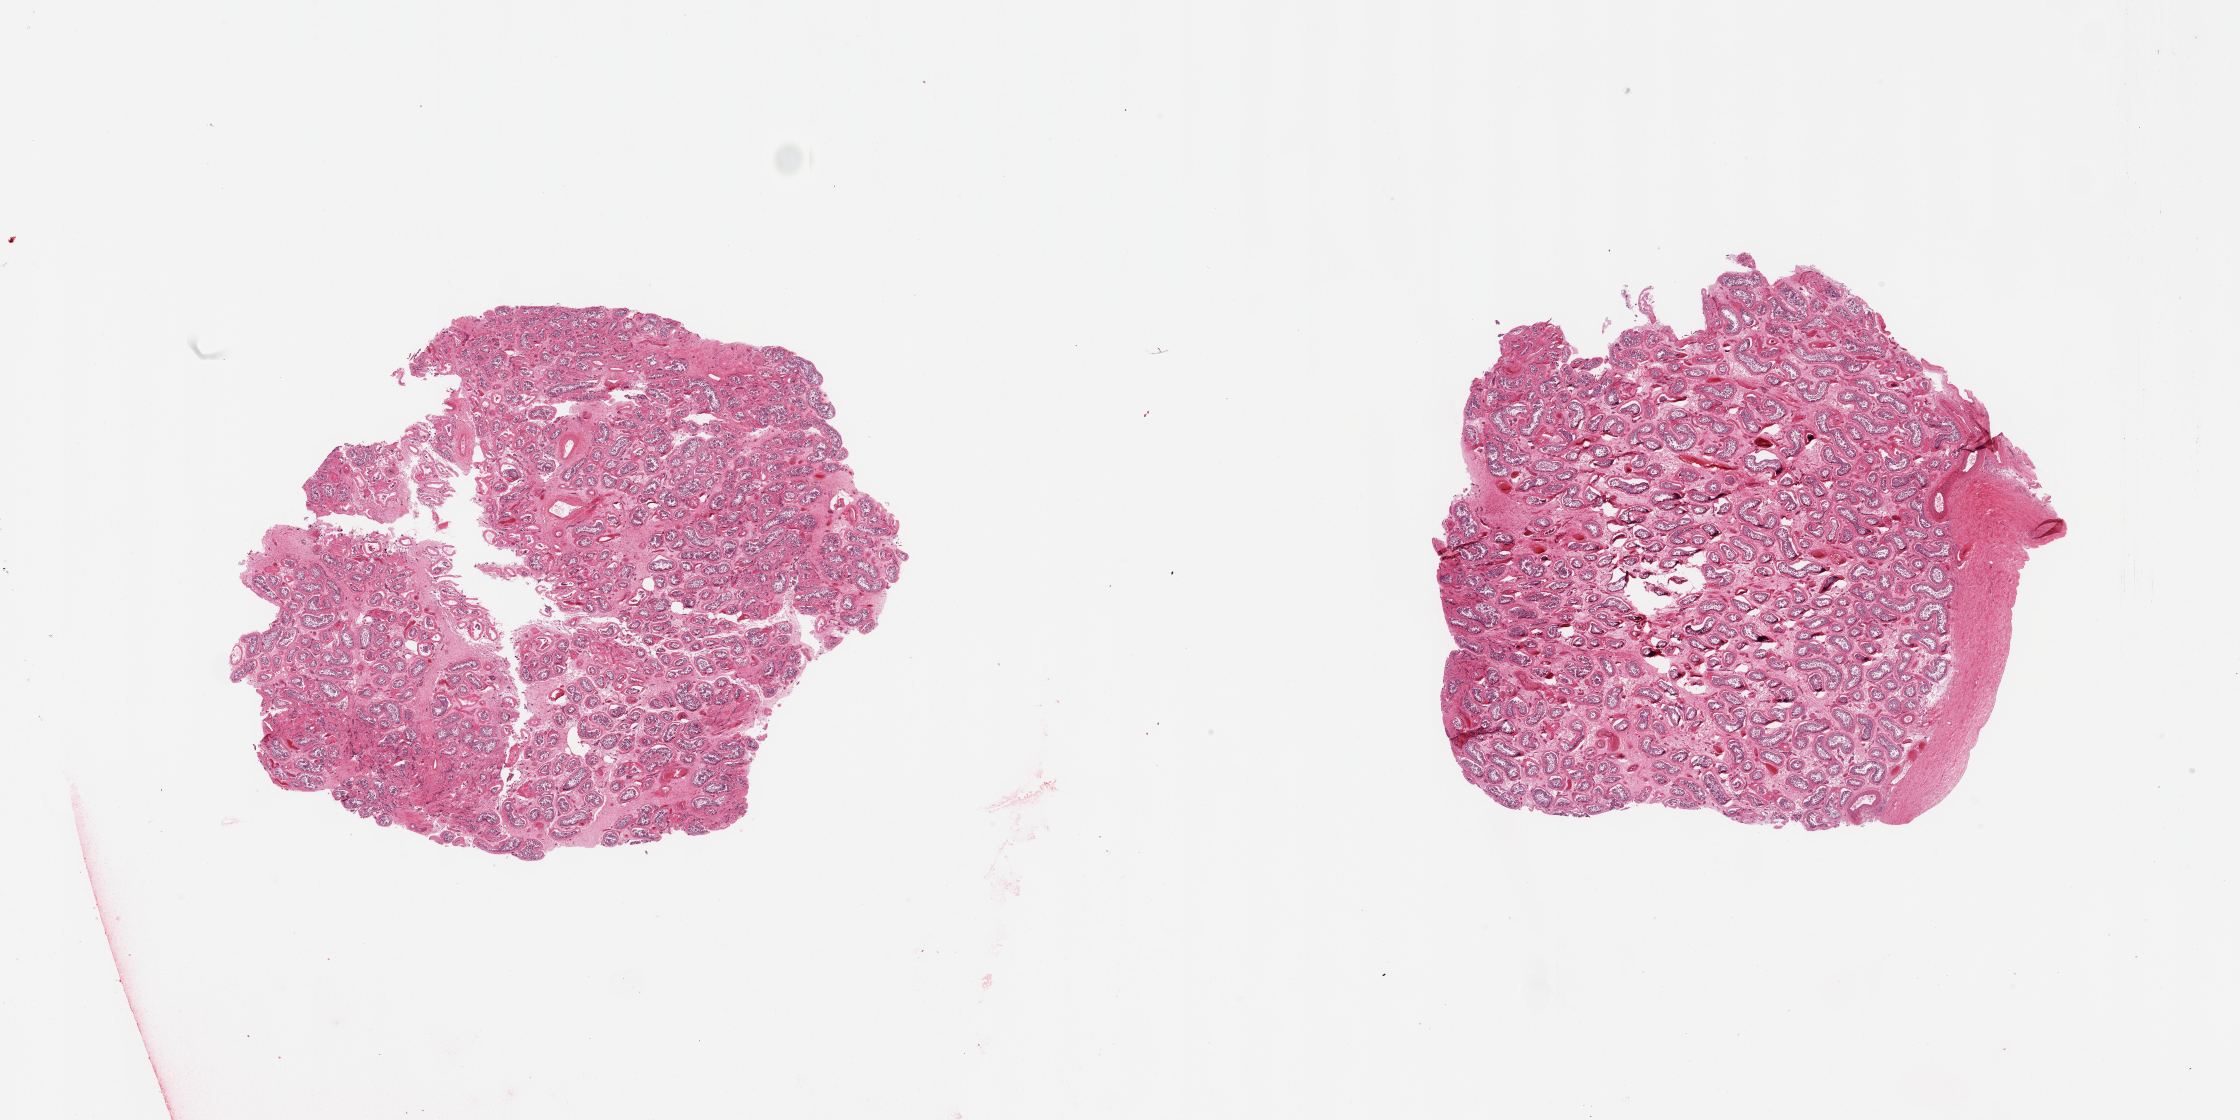
Haematoxylin and eosin whole-slide image — a low-resolution overview of the entire scanned area, about 35.4 x 17.7 mm (slide scanned at 20x); PAXgene-fixed paraffin-embedded (PFPE) section; target tissue: testis; donor tissue sample. Male donor.
• reviewer comment on this tissue sample: 2 pieces; spermatogenesis present